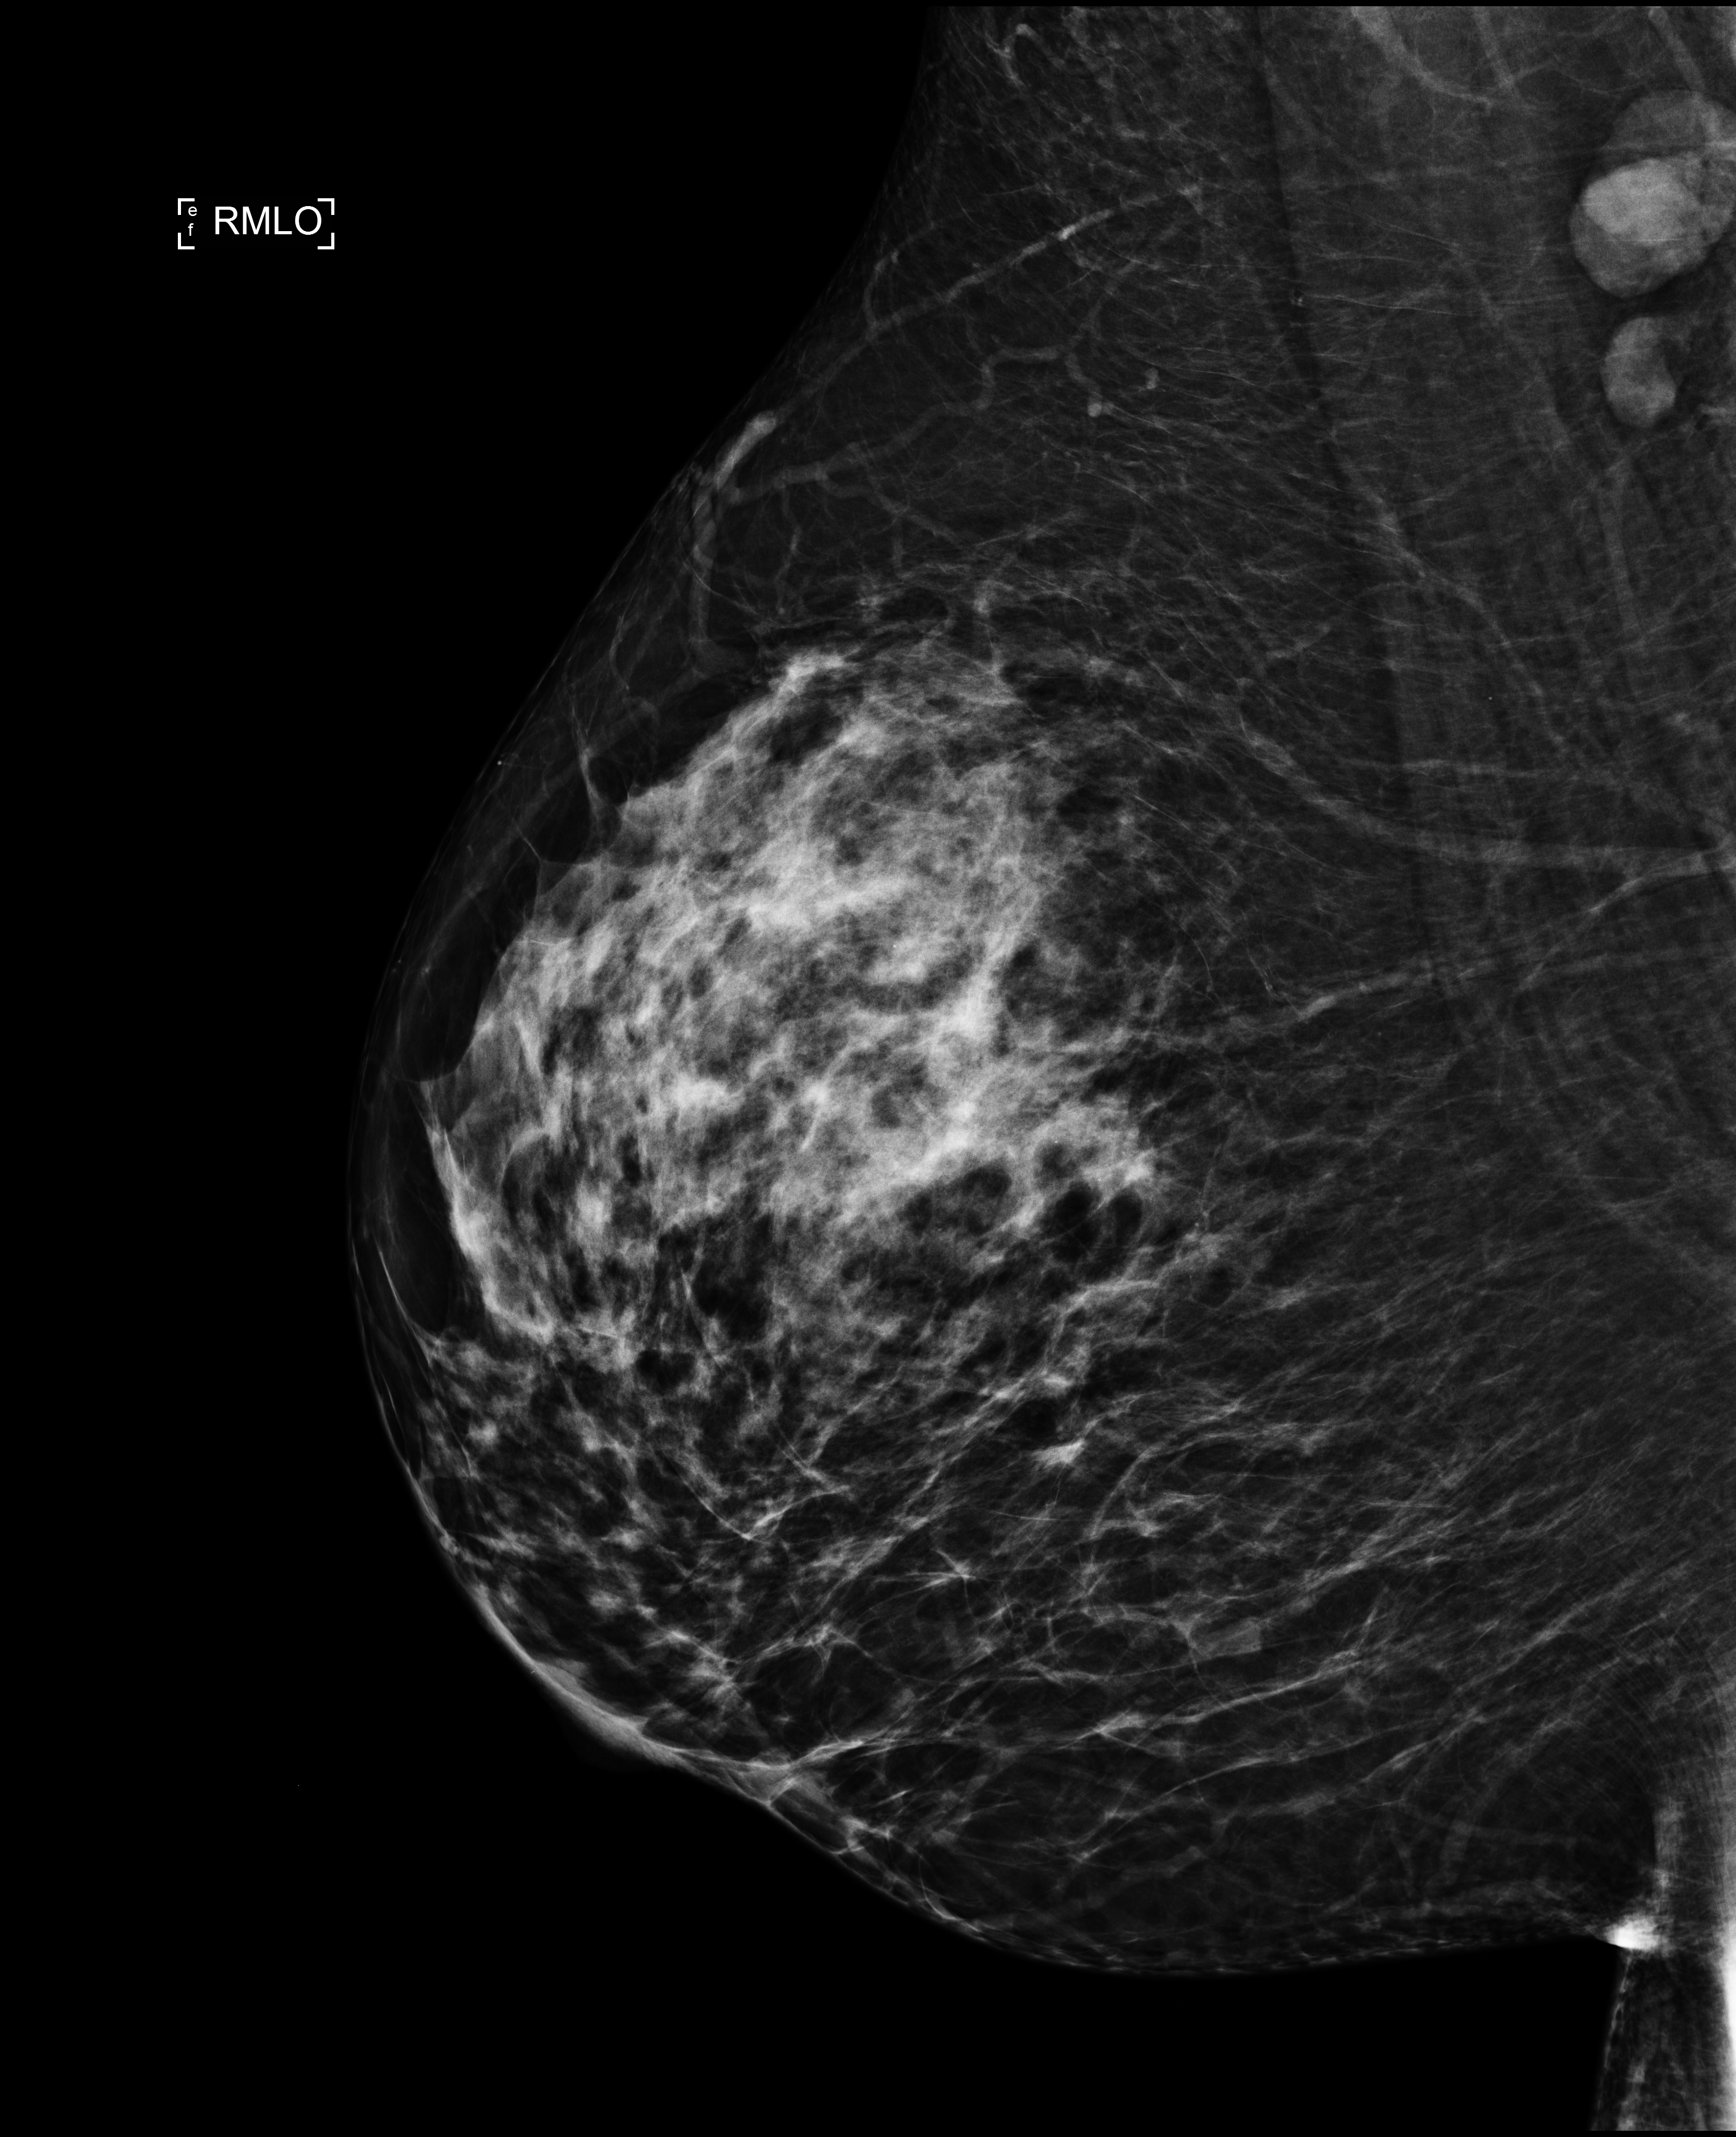
Digital mammogram (FFDM); right breast; MLO view; screening examination; compressed breast thickness 86 mm; system: Selenia Dimensions. Female patient, age 49 years.
BI-RADS breast density category at the screening exam (both breasts, scale 1–4): 3. Final BI-RADS category for the screening round (tomosynthesis exam, both breasts): category 1. Recall: no recall after this screen.